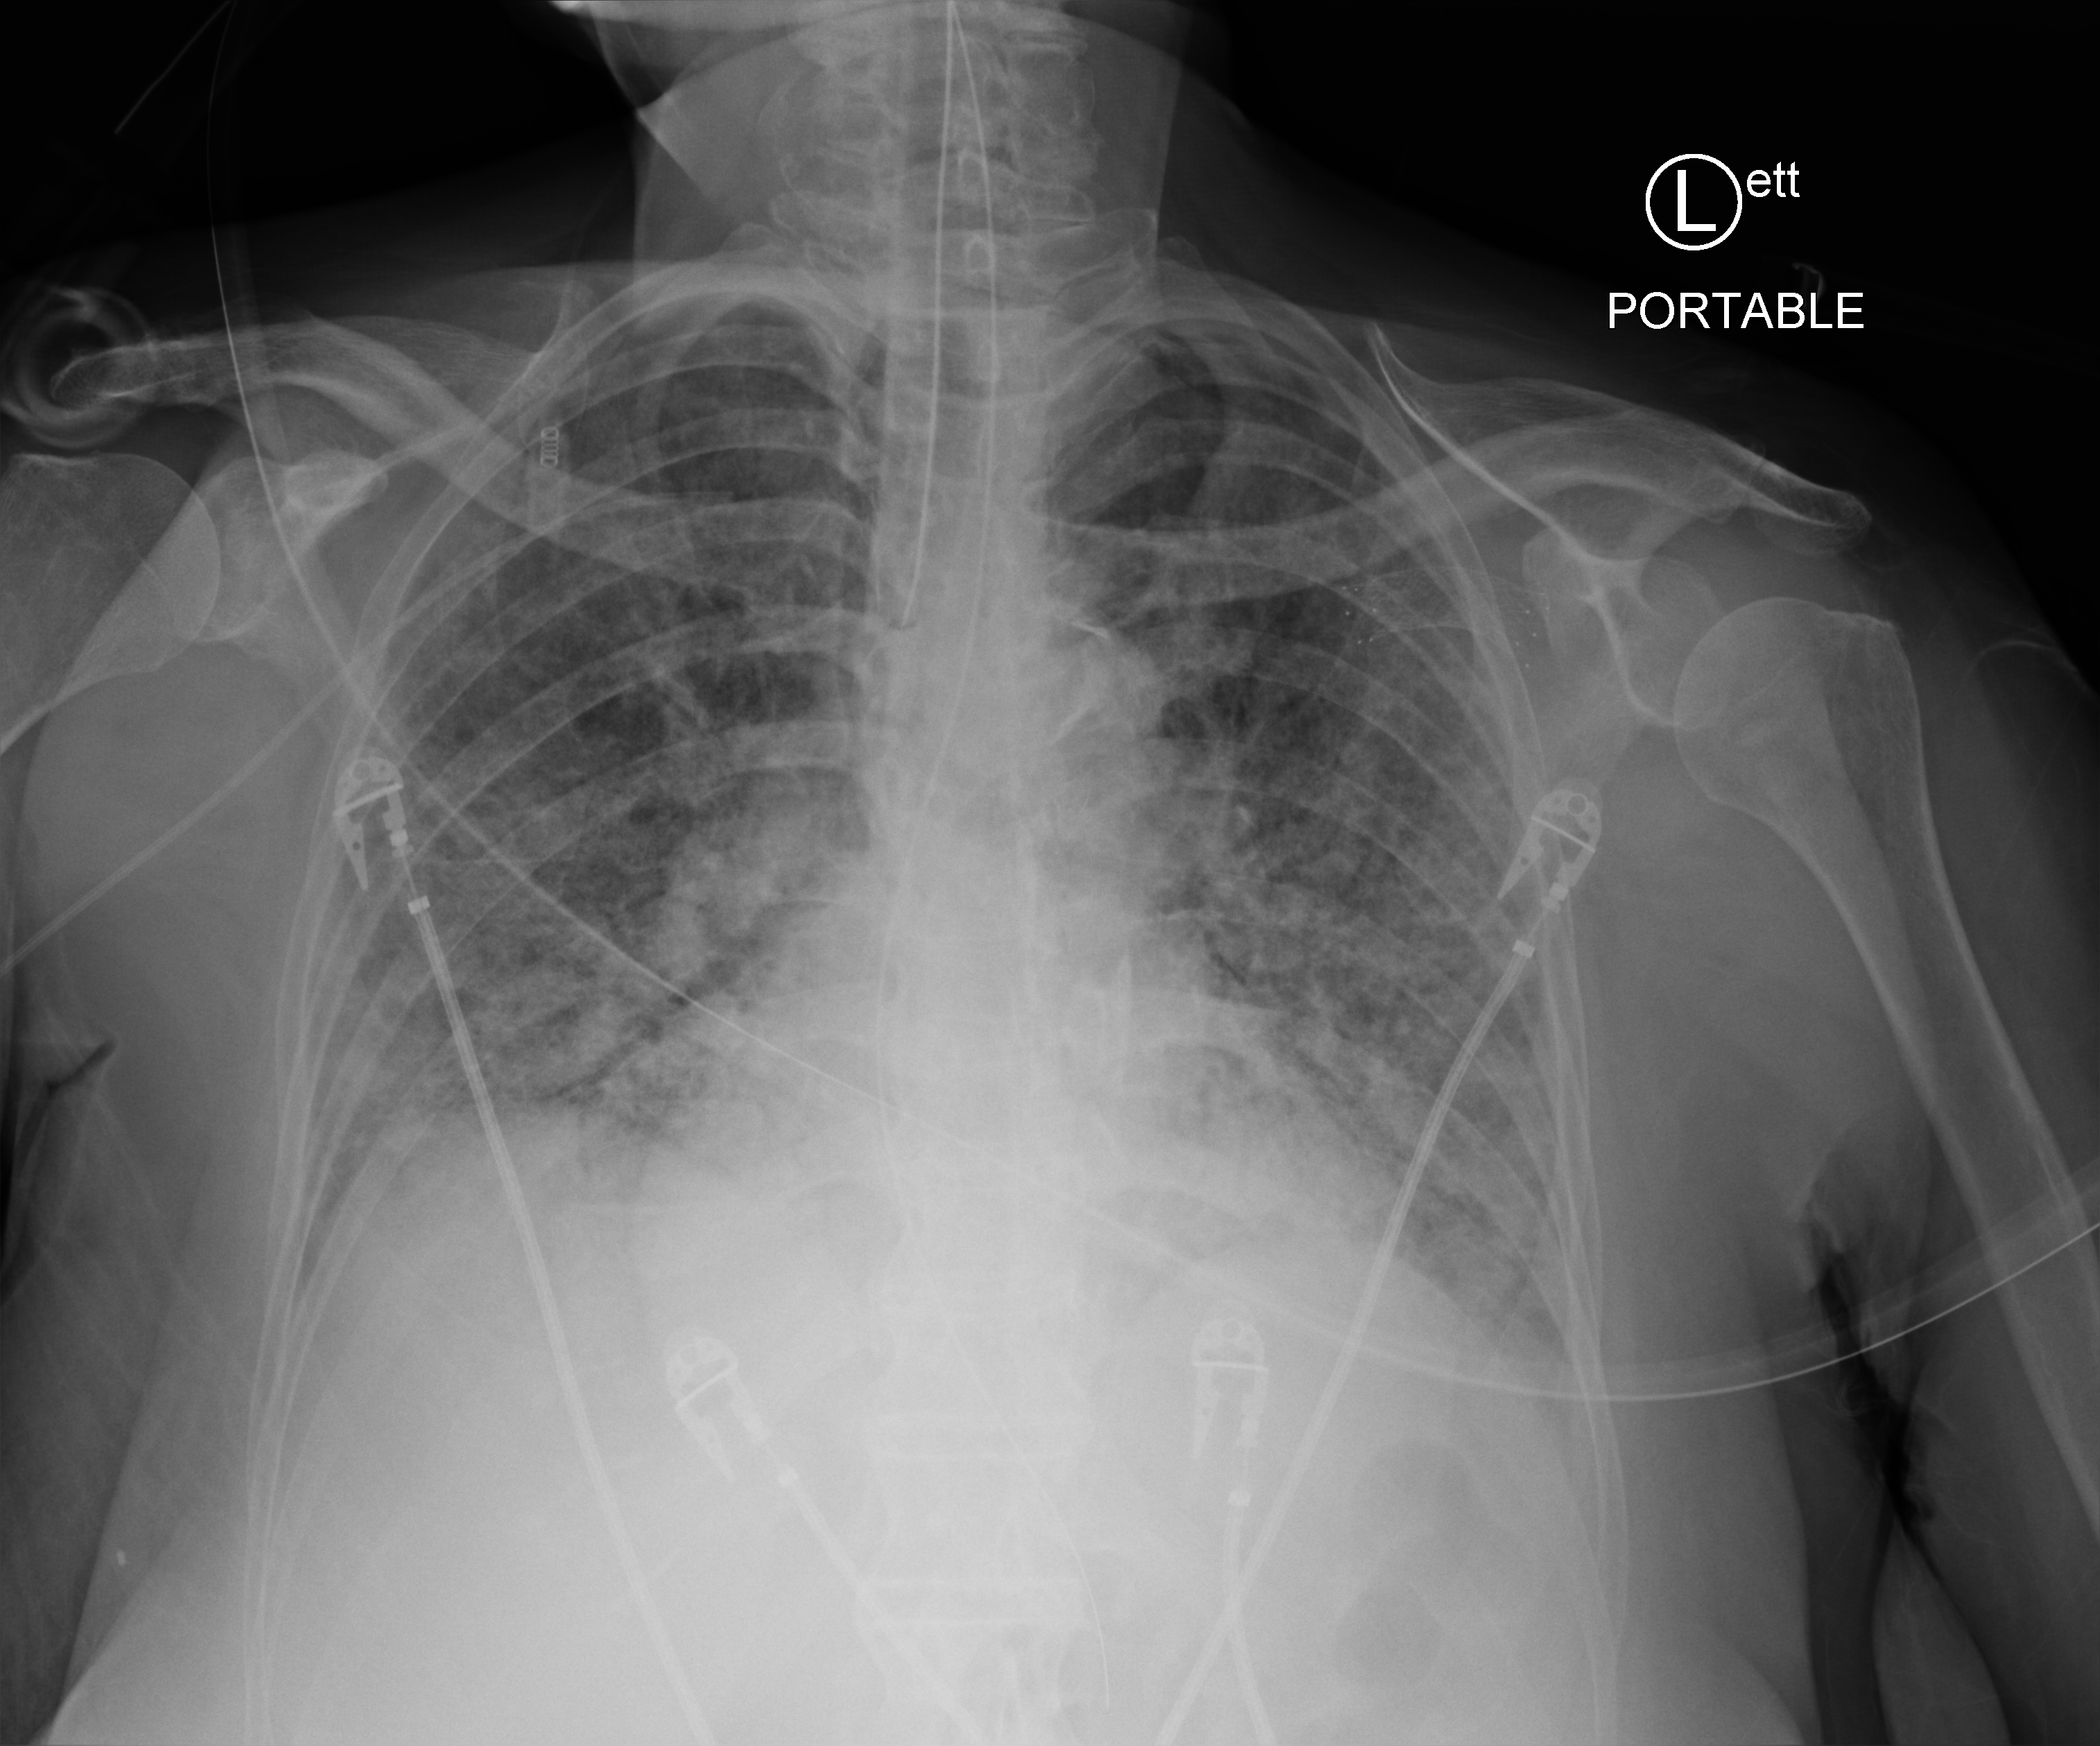
Bedside chest radiograph (computed radiography), anteroposterior (AP) projection. Female patient hospitalised with COVID-19, age 60–74 years.
From the hospital-stay record, not from the radiograph (when in the stay this image was taken is not recorded): hypertension (admission record): yes.